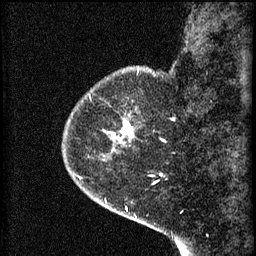
Breast MRI (dynamic contrast-enhanced), one sagittal slice. Position 11 of 60 along the scan axis. 3 images stored at this slice position (order not interpretable as contrast timing). 1.5 T. TE 4.2 ms, TR 8.2 ms. 2 mm slice thickness. 256 × 256 image matrix, field of view 180 × 180 mm. Patient: female, 44 years.
Structures marked on this image (semi-automatically segmented with operator editing):
- analysis volume of interest (the breast-tissue region the enhancement analysis was run in; not a lesion): box from (x=73, y=86) to (x=139, y=159) px
- tumour enhancement mask (voxels above the 70 % enhancement threshold inside the analysis volume of interest): (x=111, y=122)–(x=134, y=151)